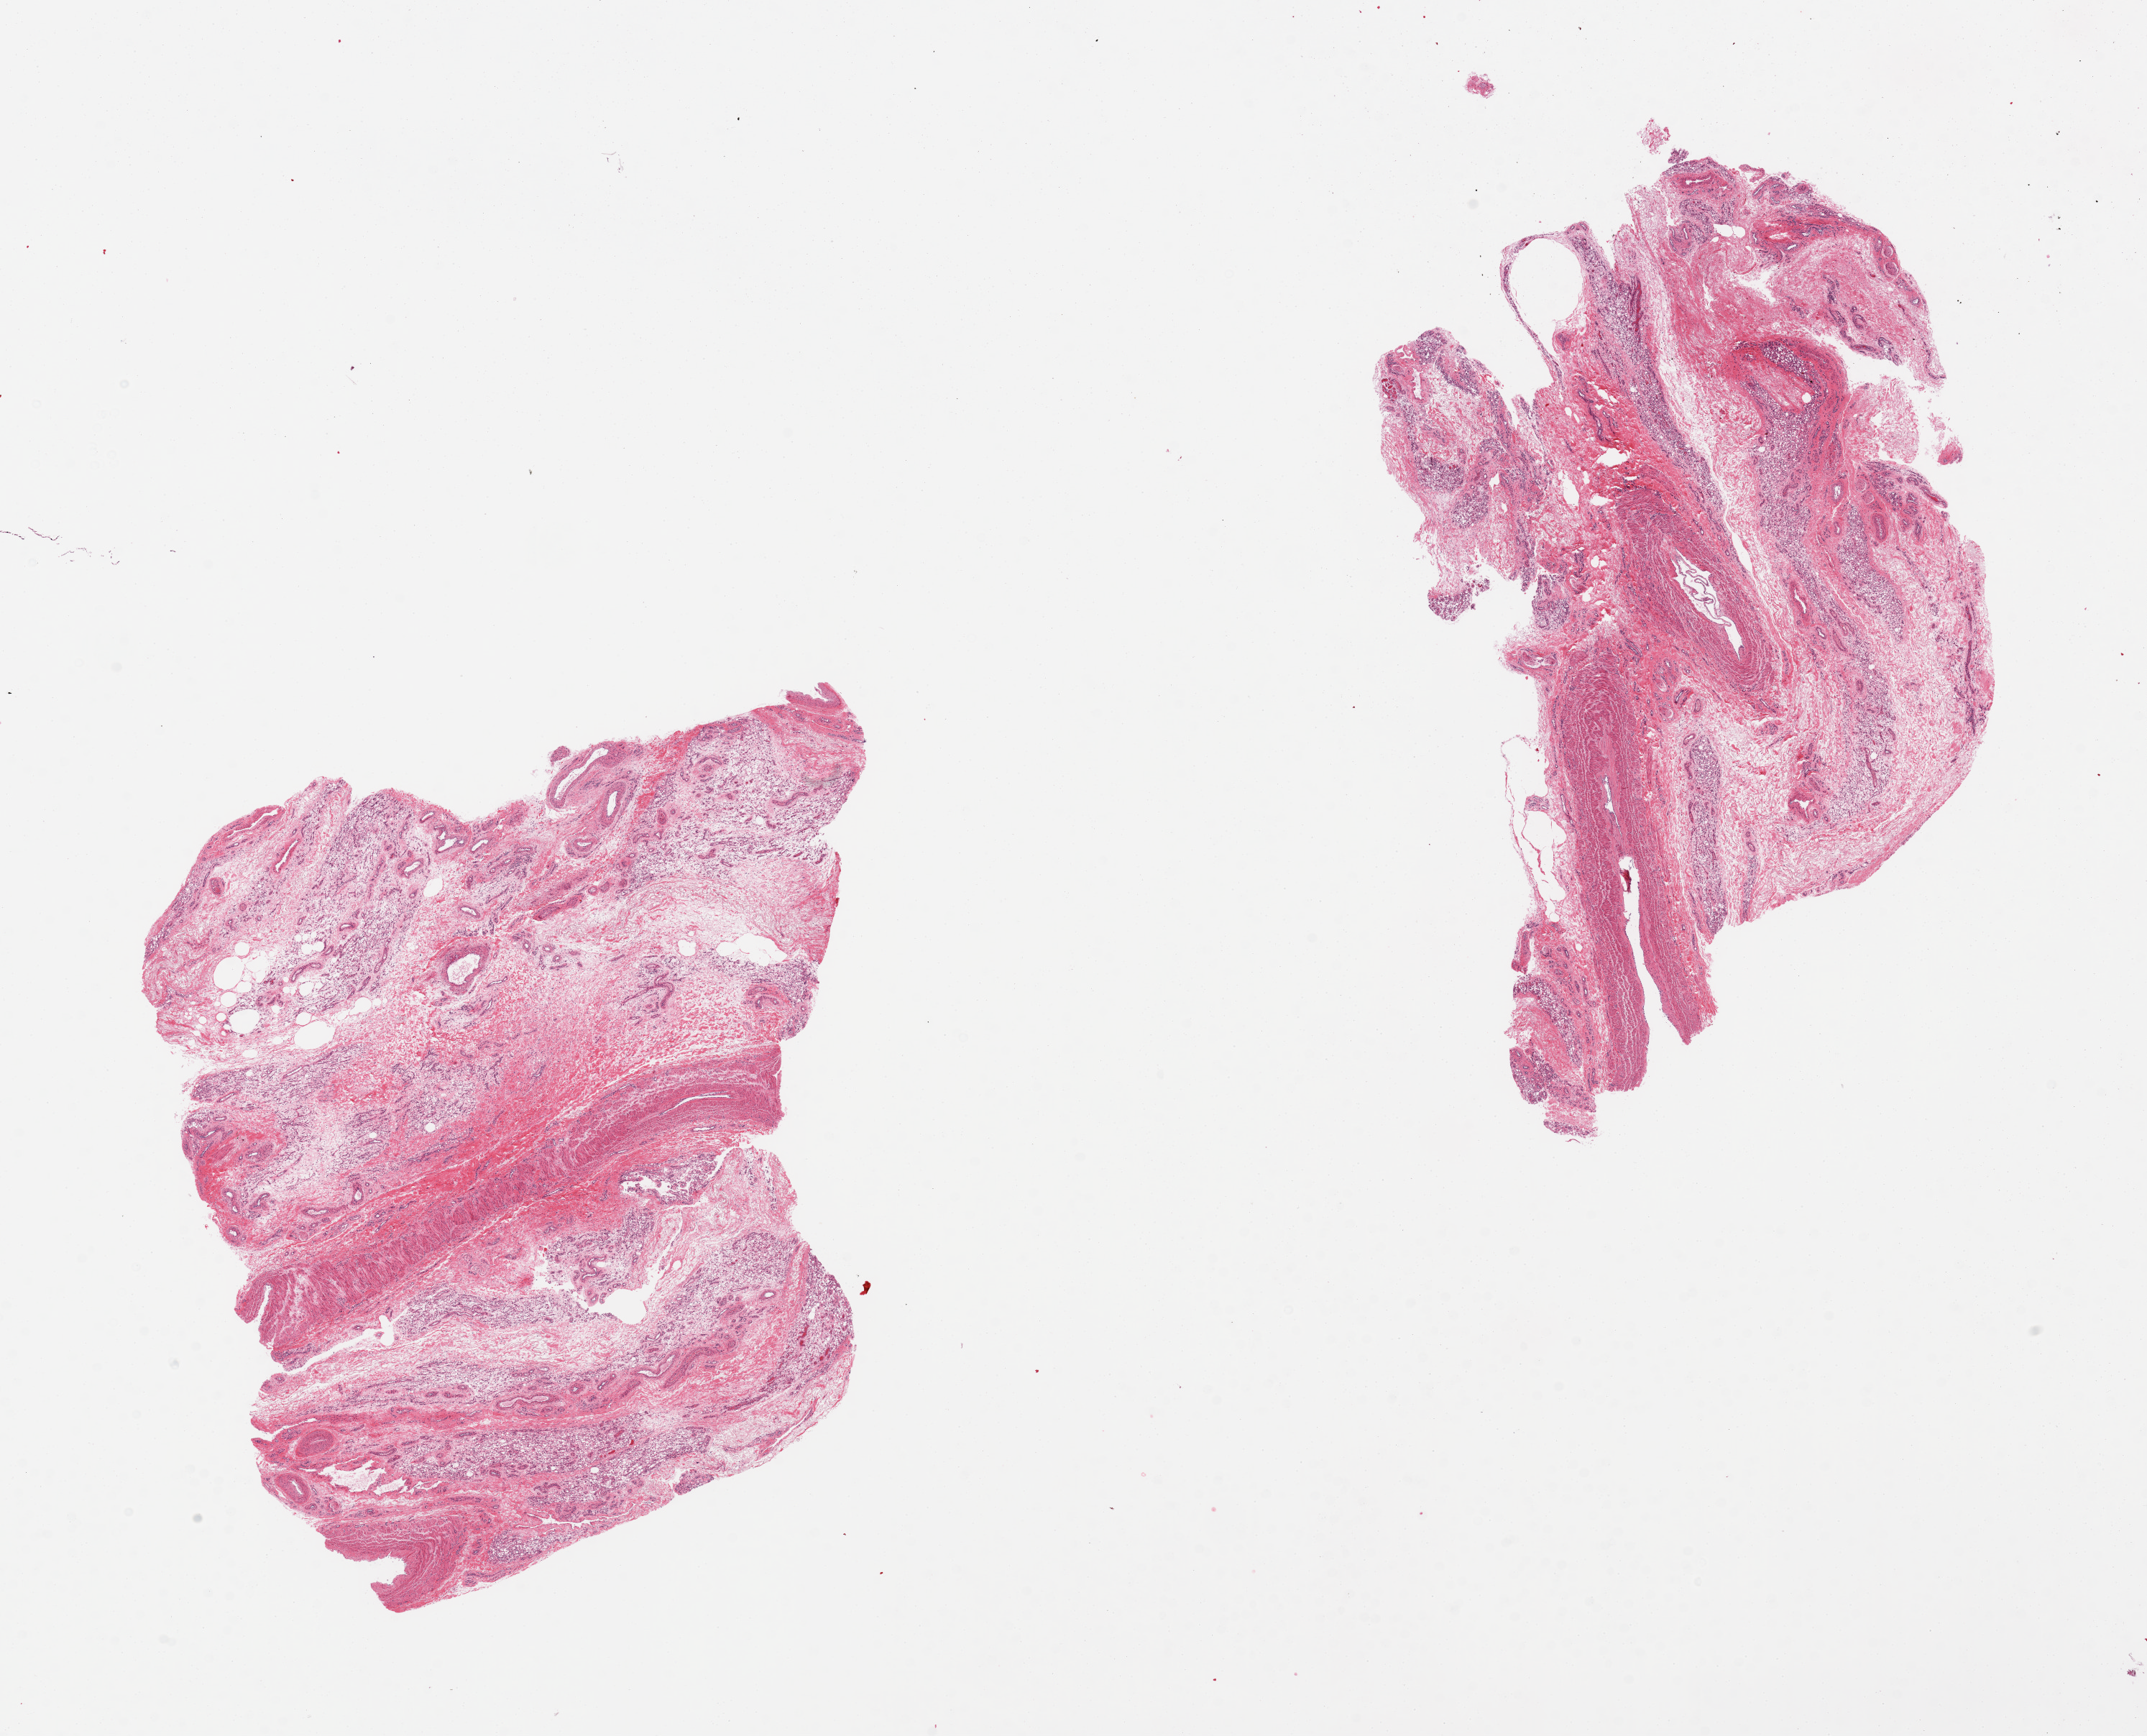
Whole-slide image, haematoxylin and eosin stain, brightfield — a low-resolution overview of the entire scanned area, about 23.6 x 19.1 mm (from a 20x scan), PAXgene-fixed paraffin-embedded (PFPE) section, sampled site (target tissue): adipose tissue, tissue donor sample. Donor: male.
Pathologist's review note for this sample: 2 pieces, fibroconnective and vascular tissue, minimal adipose tissue; unknown provenenance.